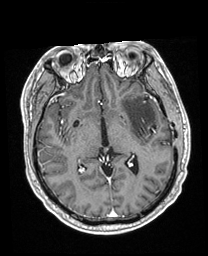
Brain MRI from a brain-tumour surgery series, one axial slice. Position 112 of 208 along the scan axis. T1-weighted post-contrast. 1 mm slice thickness. 208 × 256 image matrix, field of view 211 × 260 mm. From the clinical record (not read from this slice): histopathology: Astrocytoma; WHO grade: 3; IDH mutation: yes; tumour location: Left Insular.
Outlined on this slice (outlined manually by an expert reader):
- previous resection cavity: box from (x=150, y=125) to (x=156, y=134) px